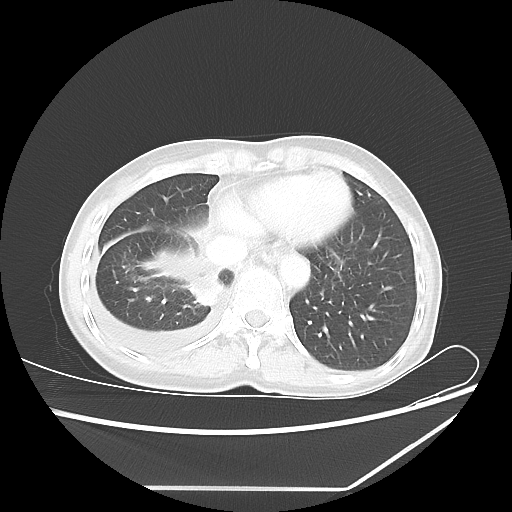
Chest CT, one axial slice. Slice 17 of 60 in the series (ordered by position). Reconstruction kernel LUNG. 80 kVp. Lung window (W 1500 / L -600 HU). 5 mm slice thickness. 512 × 512 image matrix, field of view 364 × 364 mm. Female patient, age 59 years. Case-level facts recorded for this patient, not image findings: clinical TNM (as recorded): T1c N1 M1.
Structures marked on this image (rectangle marked by the reading radiologist):
- lung tumour (recorded histology: adenocarcinoma): bounding box <186,275,224,307> (left, top, right, bottom; pixels)